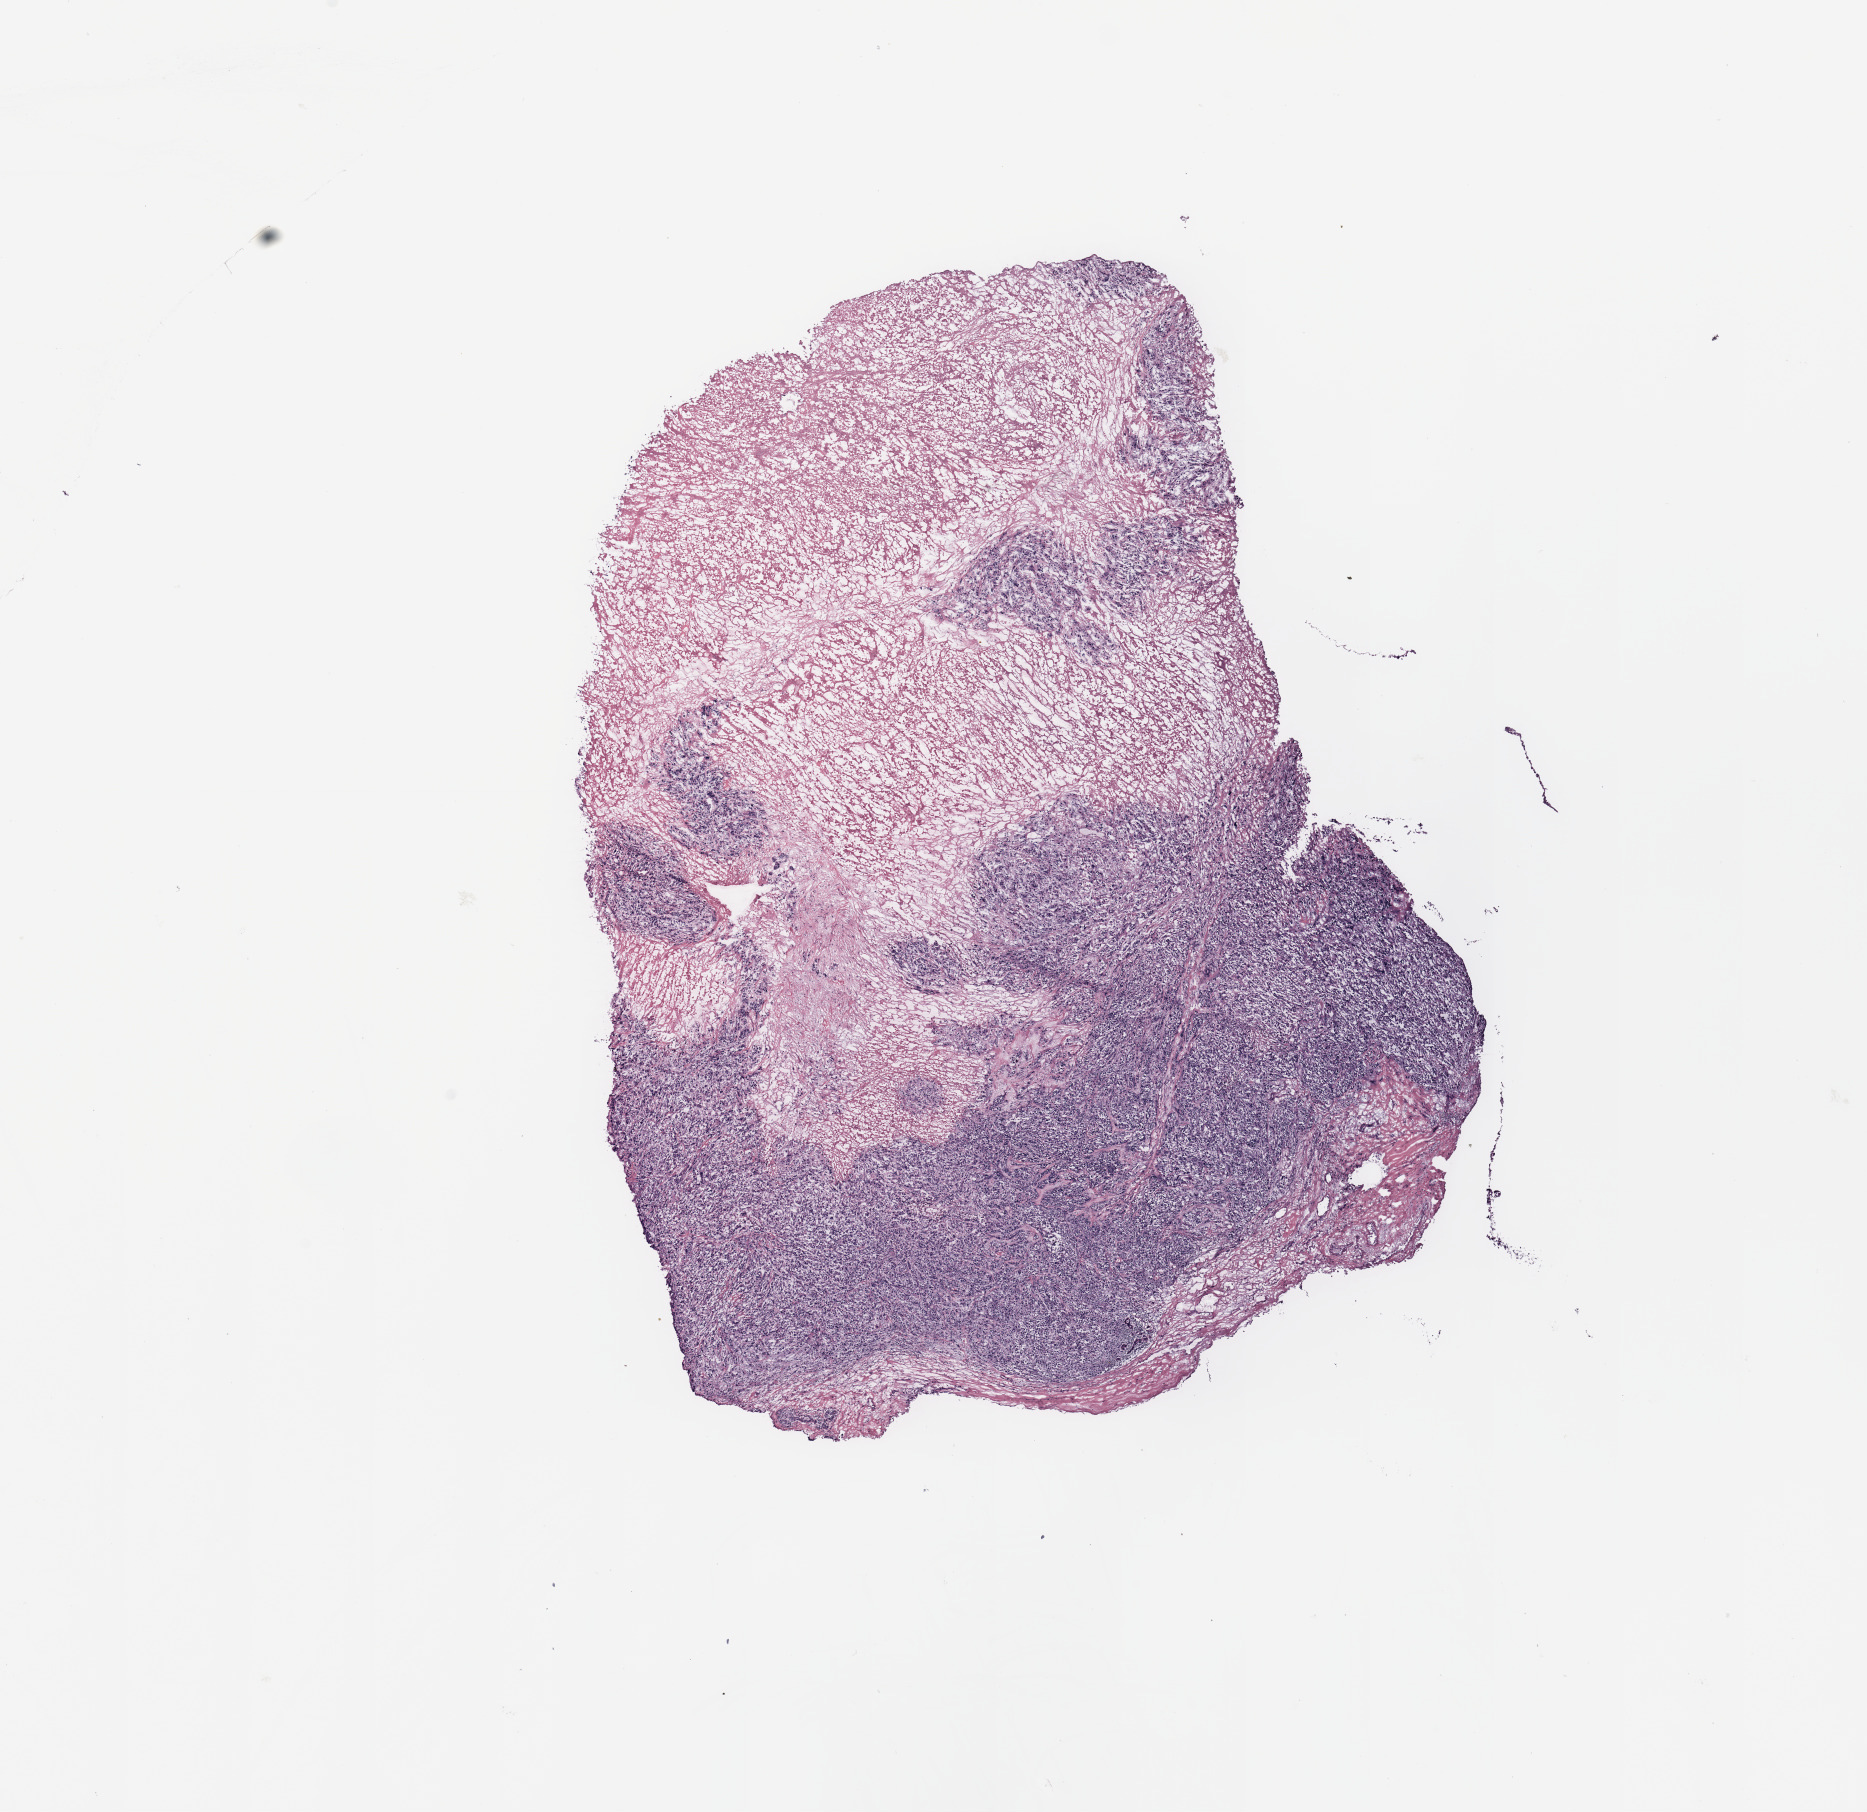
Whole-slide histology image, H&E-stained — shown as a low-resolution overview of the whole scanned area (about 14.8 x 14.3 mm), breast, tissue type not recorded. Female, 65 y/o.
* patient diagnosis: Infiltrating duct carcinoma, NOS